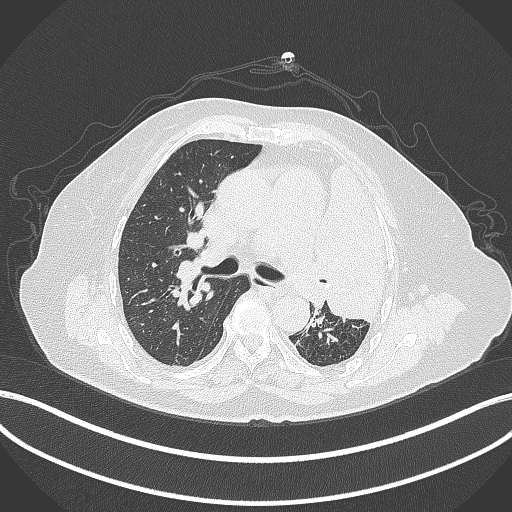
Chest CT, one axial slice; slice 242 of 399 in the series (ordered by position); reconstruction kernel B70f; 120 kVp; lung window (W 1500 / L -600 HU); 1 mm slice thickness; 512 × 512 image matrix. Female patient, age 75 years. From the clinical record (not read from this slice): clinical TNM (as recorded): T3 N3 M1.
Structures marked on this image (rectangle marked by the reading radiologist):
- lung tumour (recorded histology: adenocarcinoma): box from (x=309, y=147) to (x=401, y=328) px